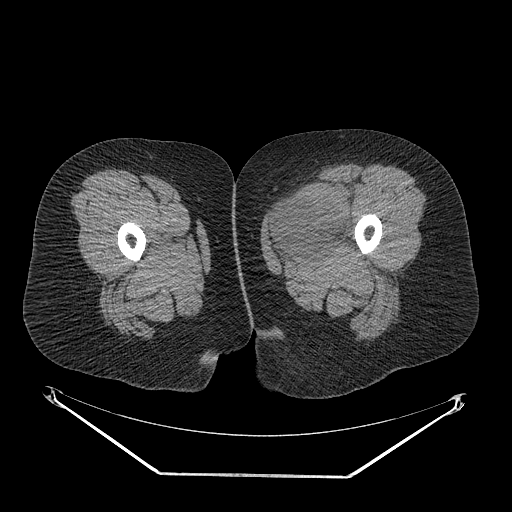
CT of an extremity soft-tissue mass (from a PET/CT study), one axial slice; slice 21 of 267 in the series (ordered by position); reconstruction kernel STANDARD; 140 kVp; soft-tissue window (W 400 / L 40 HU); 512 × 512 image matrix, field of view 500 × 500 mm. Female patient. Case-level facts recorded for this patient, not image findings: histological type: myxofibrosarcoma; grade: intermediate; site of the primary tumour: left thigh.
Structures marked on this image (expert contour drawn on MRI and transferred to this co-registered scan by the dataset authors):
- gross tumour volume including surrounding oedema: bounding box <269,187,353,257> (left, top, right, bottom; pixels)
- gross tumour volume (mass): <272,190,352,257>